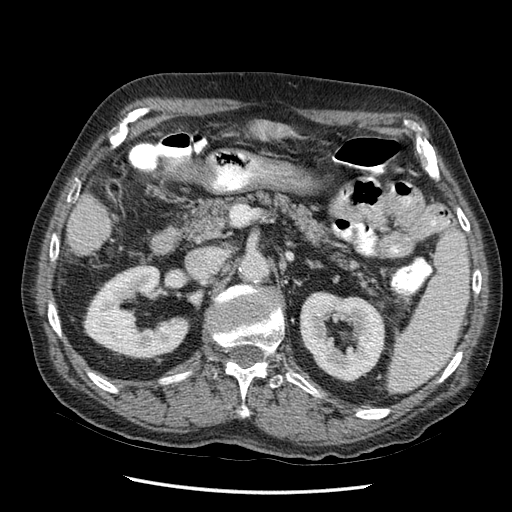
Contrast-enhanced abdominal CT (liver protocol), one axial slice; position 11 of 67 along the scan axis; reconstruction kernel STANDARD; 120 kVp; soft-tissue window (W 400 / L 40 HU); 512 × 512 image matrix. From the clinical record (not read from this slice): diagnosis: hepatocellular carcinoma (patient treated with transarterial chemoembolisation; whether this scan precedes or follows treatment is not stated here); TNM stage (as recorded): Stage-I; Child-Pugh class: A; tumour differentiation: moderately differentiated; tumour nodularity: uninodular.
Annotated regions visible in this slice (semi-automatic segmentation, software-assisted and operator-edited):
- liver parenchyma outside the tumour (the mass and vessels are separate outlines, so this box may not span the whole liver): box from (x=248, y=122) to (x=294, y=140) px